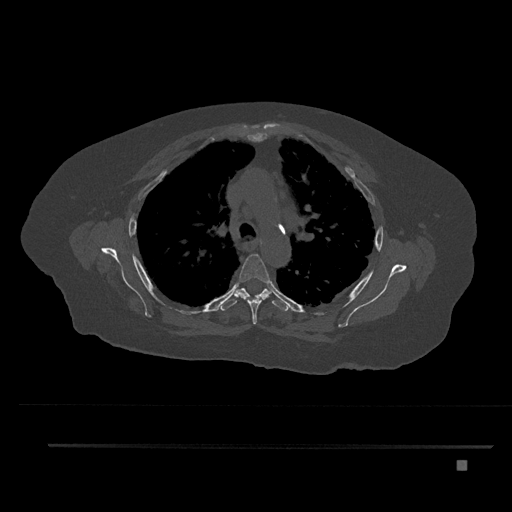
CT including the spine, one axial slice; position 589 of 797 along the scan axis; reconstruction kernel Br40s/3; 120 kVp; bone window (W 1800 / L 400 HU); 0.5 mm slice thickness; 512 × 512 image matrix. Female patient, age 76 years. From the clinical record (not read from this slice): primary cancer: lung.
Annotated regions visible in this slice (semi-automatic segmentation, software-assisted and operator-edited):
- T4 vertebra: bounding box <235,254,271,324> (left, top, right, bottom; pixels)
- T5 vertebra: <219,283,289,311>